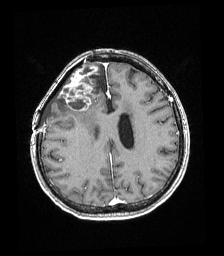
Brain MRI from a brain-tumour surgery series, one axial slice. Slice 71 of 192 in the series (ordered by position). T1-weighted post-contrast. 1 mm slice thickness. 224 × 256 image matrix. Case-level facts recorded for this patient, not image findings: histopathology: Astrocytoma; WHO grade: 4; IDH mutation: yes.
Annotated regions visible in this slice (outlined manually by an expert reader):
- tumour: box from (x=60, y=62) to (x=98, y=112) px